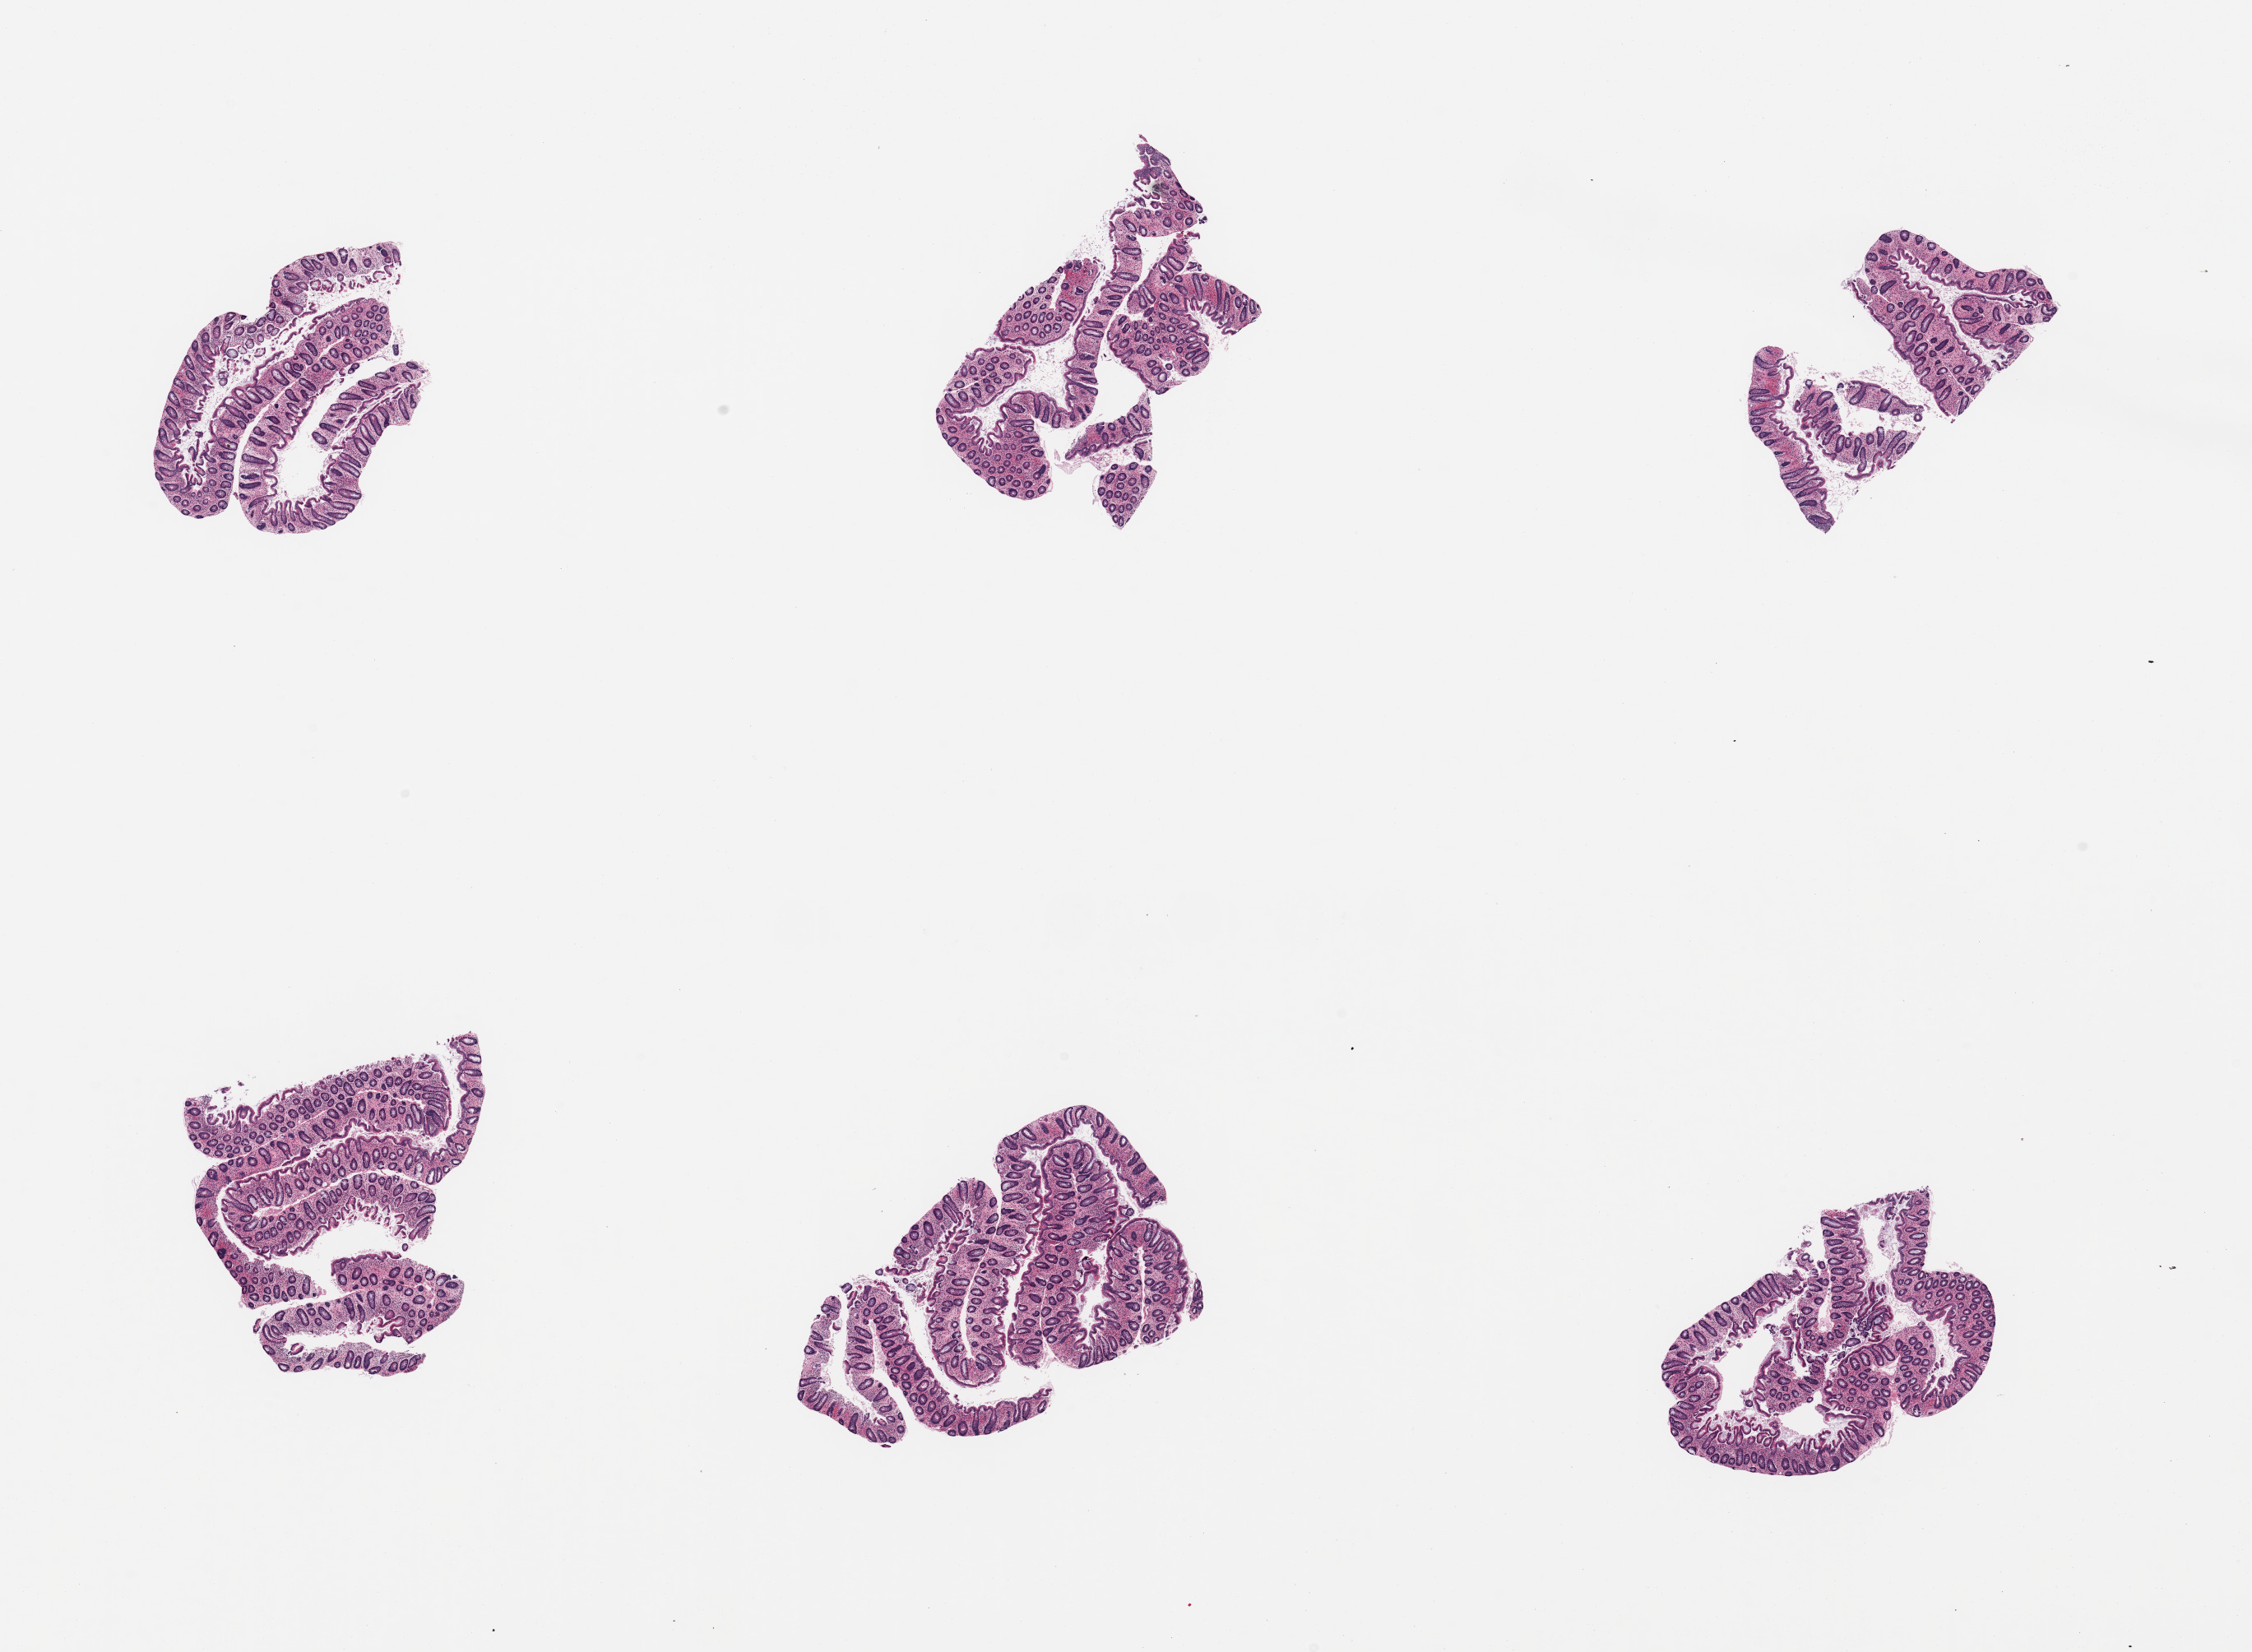
Digitized haematoxylin and eosin-stained section, brightfield — low-resolution overview of the scanned area, about 21.7 x 15.9 mm (slide scanned at 20x); PAXgene-fixed paraffin-embedded (PFPE) section; target tissue: transverse colon; tissue donor sample. Donor: female.
Review note (as recorded): 6 pieces; mucosa only, some superficial hemorrhage.